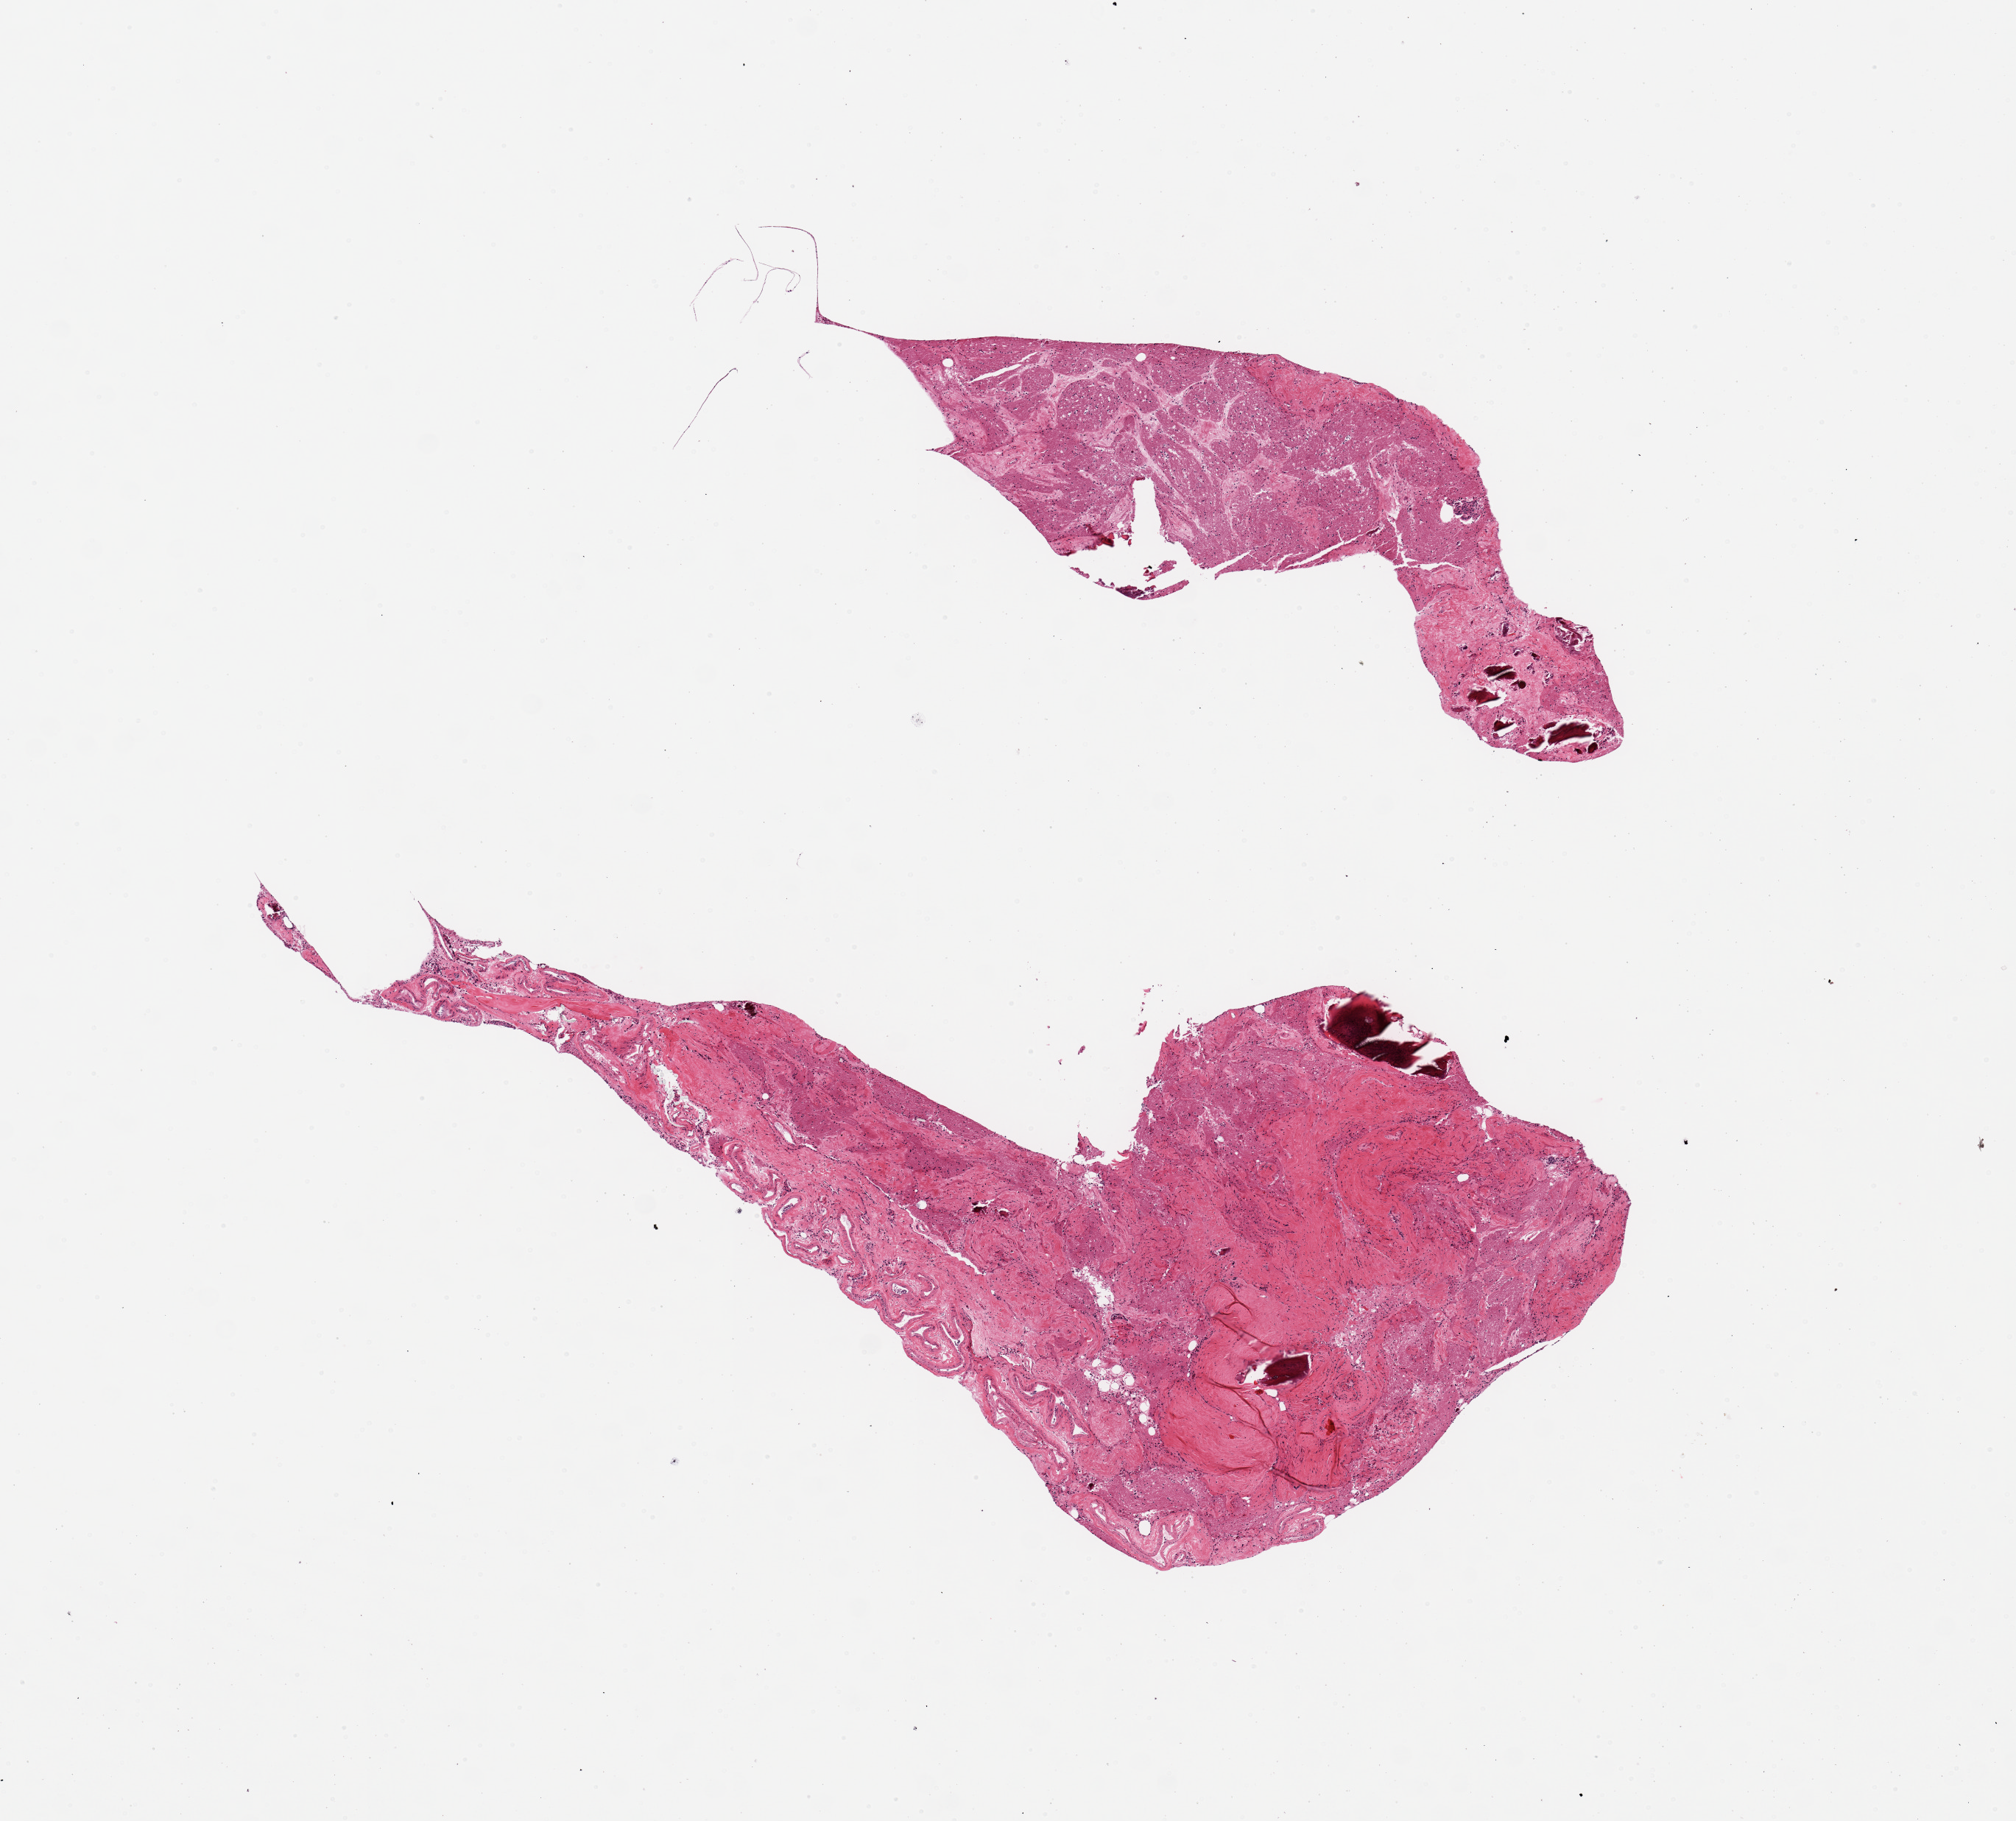
Whole-slide image, haematoxylin and eosin stain, a low-resolution overview of the entire scanned area, about 10.8 x 9.8 mm (acquisition: 20x scan); PAXgene-fixed paraffin-embedded (PFPE) section; target tissue: pituitary; tissue donor sample. Donor sex: female.
Review note (as recorded): 2 pieces, marked autolysis, calcified debris/fibrous tissue/delineted in ~49% of specimen.